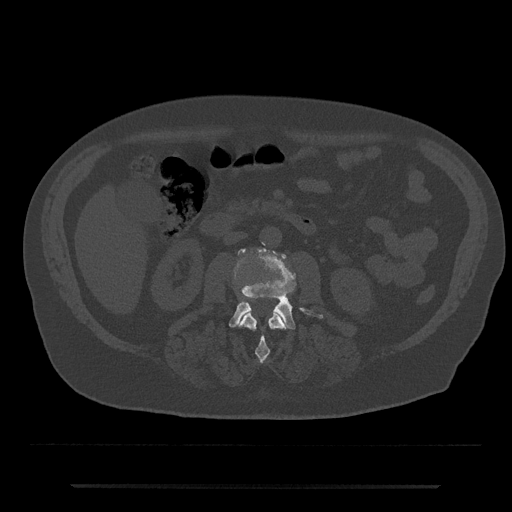
CT including the spine, one axial slice. Slice 435 of 797 in the series (ordered by position). Bone window (W 1800 / L 400 HU). 512 × 512 image matrix, field of view 434 × 434 mm. Patient: male, 80 years. Case-level facts recorded for this patient, not image findings: primary cancer: prostate; vertebrae with lytic lesions (as recorded): L1, T11.
Outlined on this slice (semi-automatic segmentation, software-assisted and operator-edited):
- L2 vertebra: bounding box [x1, y1, x2, y2] px = [240, 310, 286, 363]
- L3 vertebra: [229, 248, 323, 329]